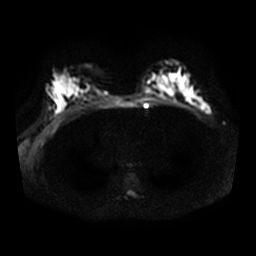
Breast MRI, one axial slice. Diffusion-weighted series; image 2 of 4 stored at this slice position (different b-values; order by instance number). 3 T. 256 × 256 image matrix, field of view 340 × 340 mm. Female patient.
Structures marked on this image (outlined manually by an expert reader):
- tumour on diffusion-weighted imaging: bounding box <201,103,210,113> (left, top, right, bottom; pixels)